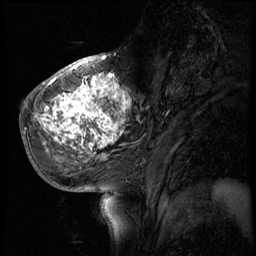
Breast MRI (dynamic contrast-enhanced), one sagittal slice; slice 24 of 56 in the series (ordered by position); 4 images stored at this slice position (order not interpretable as contrast timing); 1.5 T; TE 4.2 ms, TR 8.9 ms; 256 × 256 image matrix. Female patient, age 51 years. From the clinical record (not read from this slice): setting: breast cancer imaged before/during neoadjuvant chemotherapy; receptor status: triple-negative.
Annotated regions visible in this slice (semi-automatic segmentation, software-assisted and operator-edited):
- analysis volume of interest (the breast-tissue region the enhancement analysis was run in; not a lesion): bounding box (x1, y1, x2, y2) in pixels: (30, 70, 150, 173)
- tumour enhancement mask (voxels above the 140 % enhancement threshold inside the analysis volume of interest): (33, 74, 132, 153)